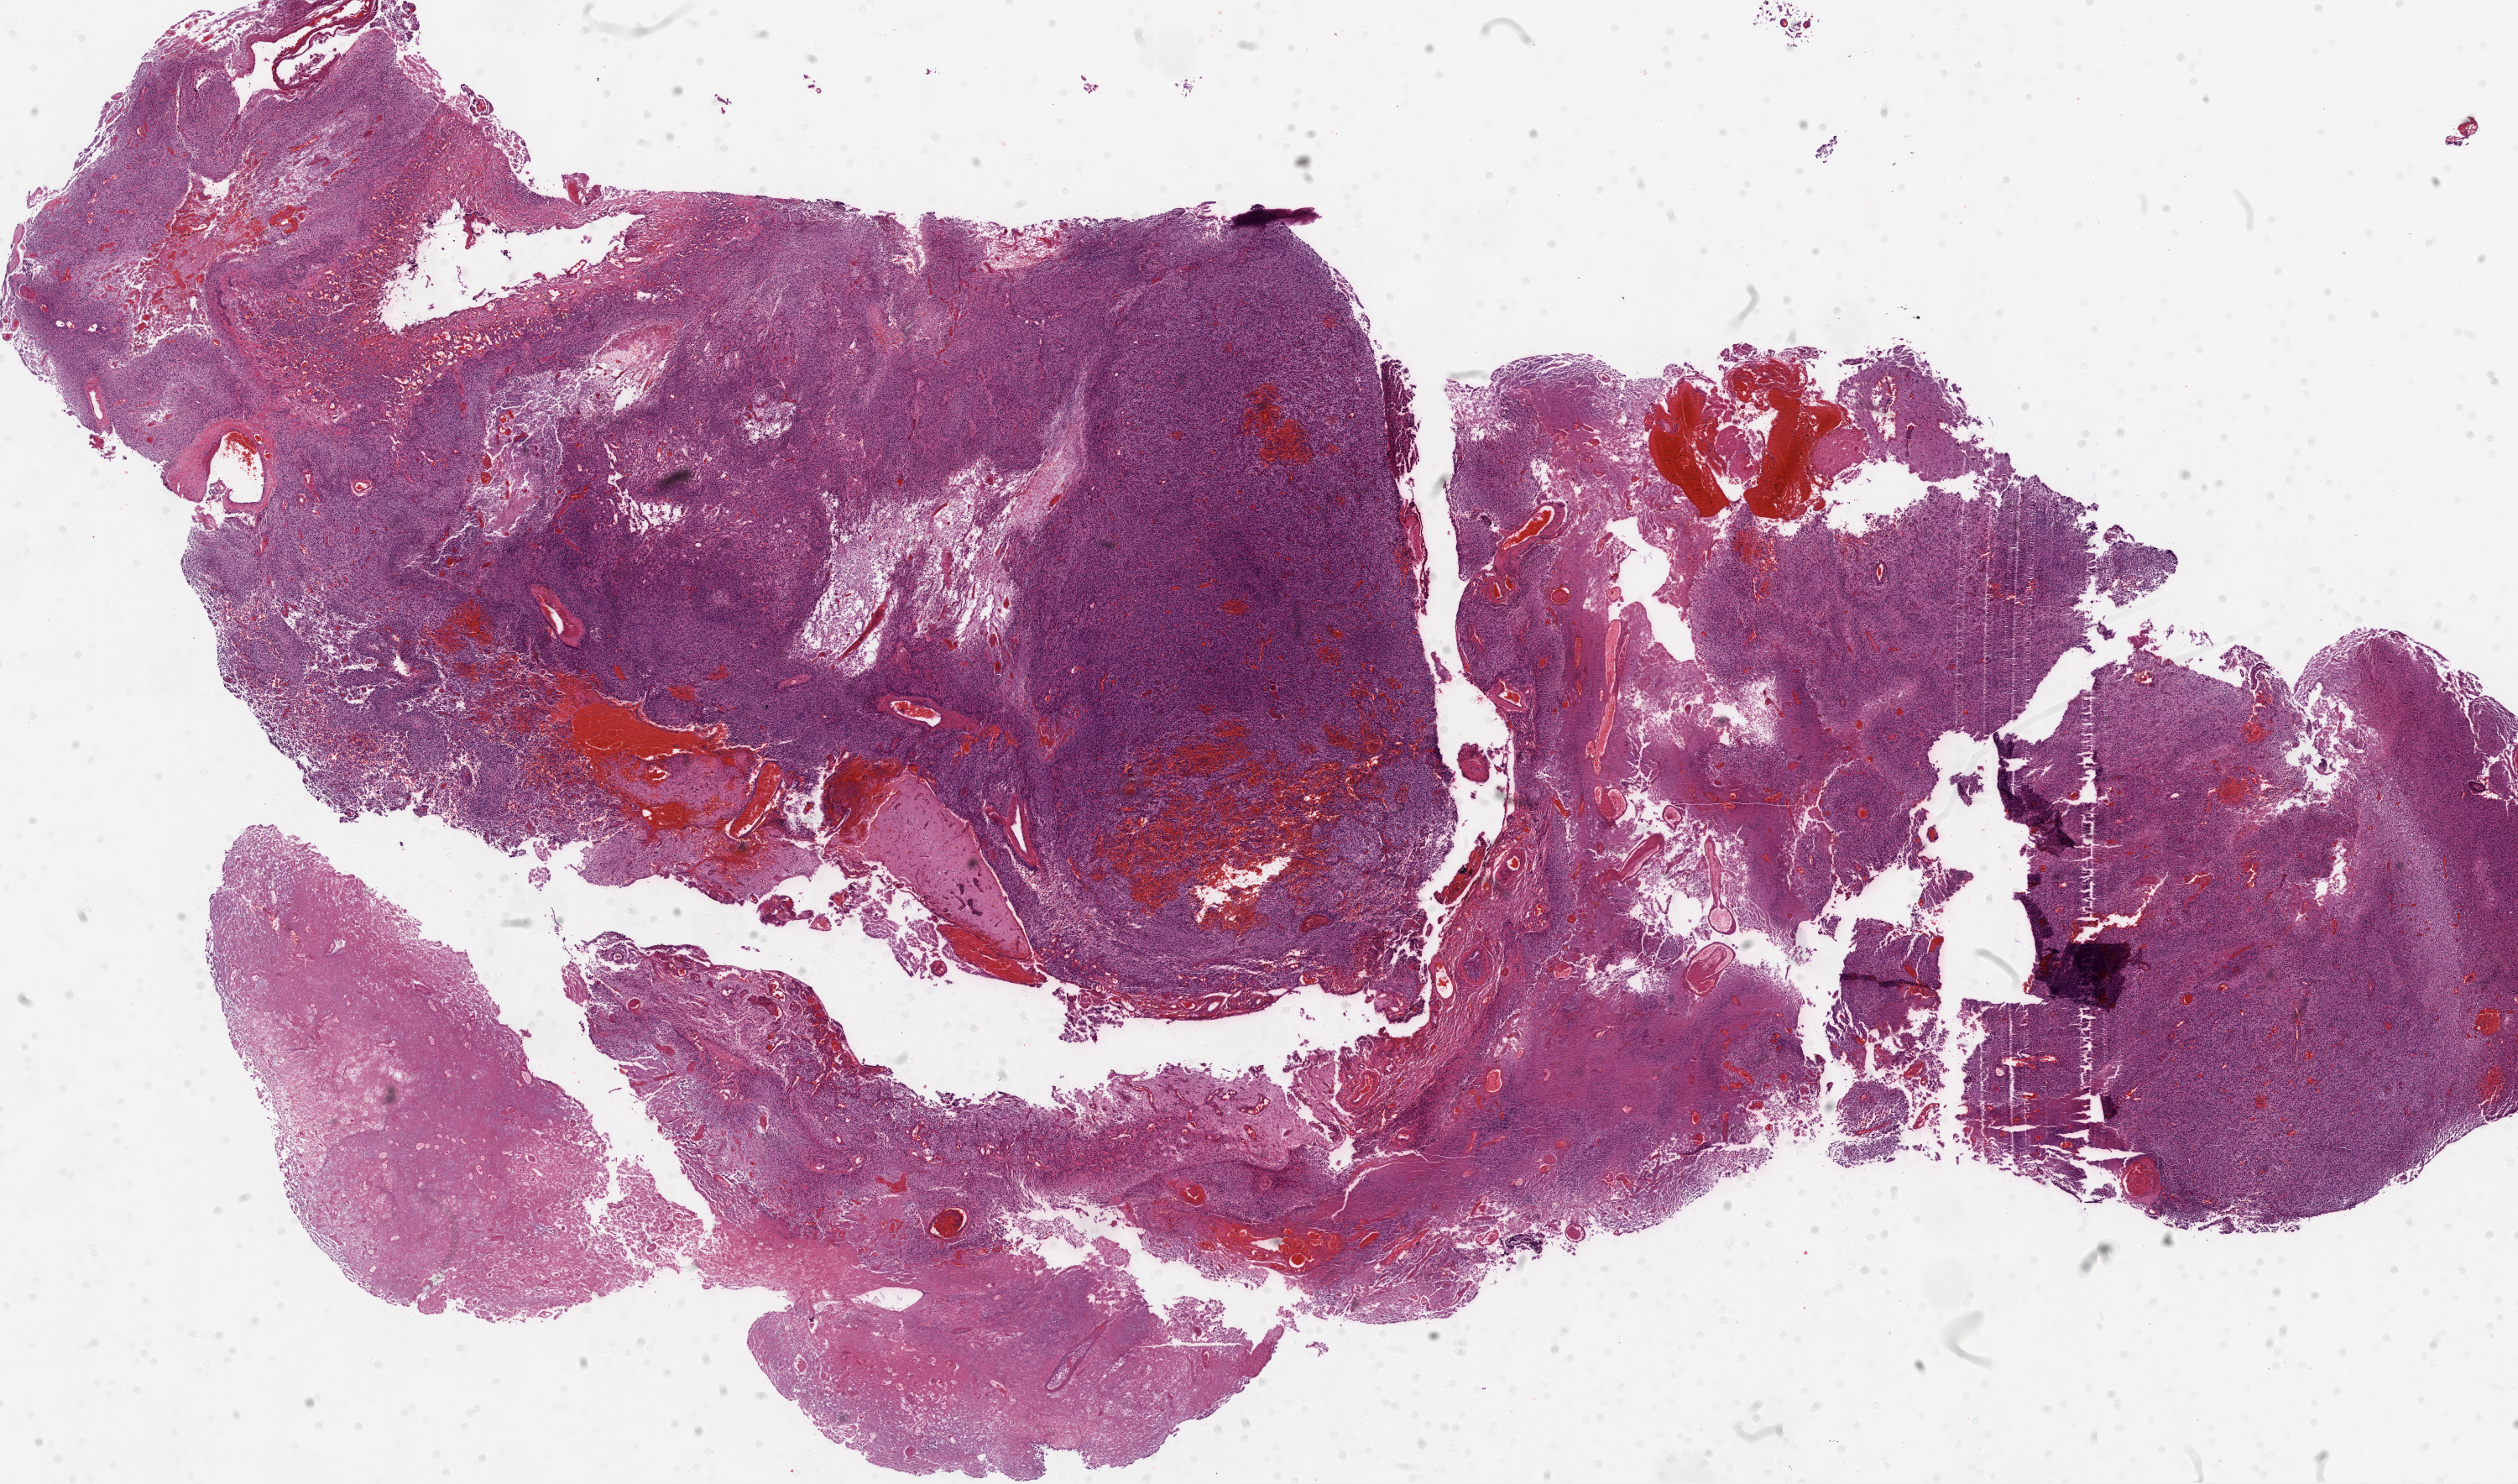
Digitized H&E tissue section (whole slide) — a low-resolution overview of the entire scanned area, about 24.1 x 14.2 mm (slide scanned at 20x); formalin-fixed paraffin-embedded (FFPE) diagnostic section; brain, primary tumour sample. Patient: female, age at initial diagnosis 77 years.
Diagnosis: Glioblastoma.